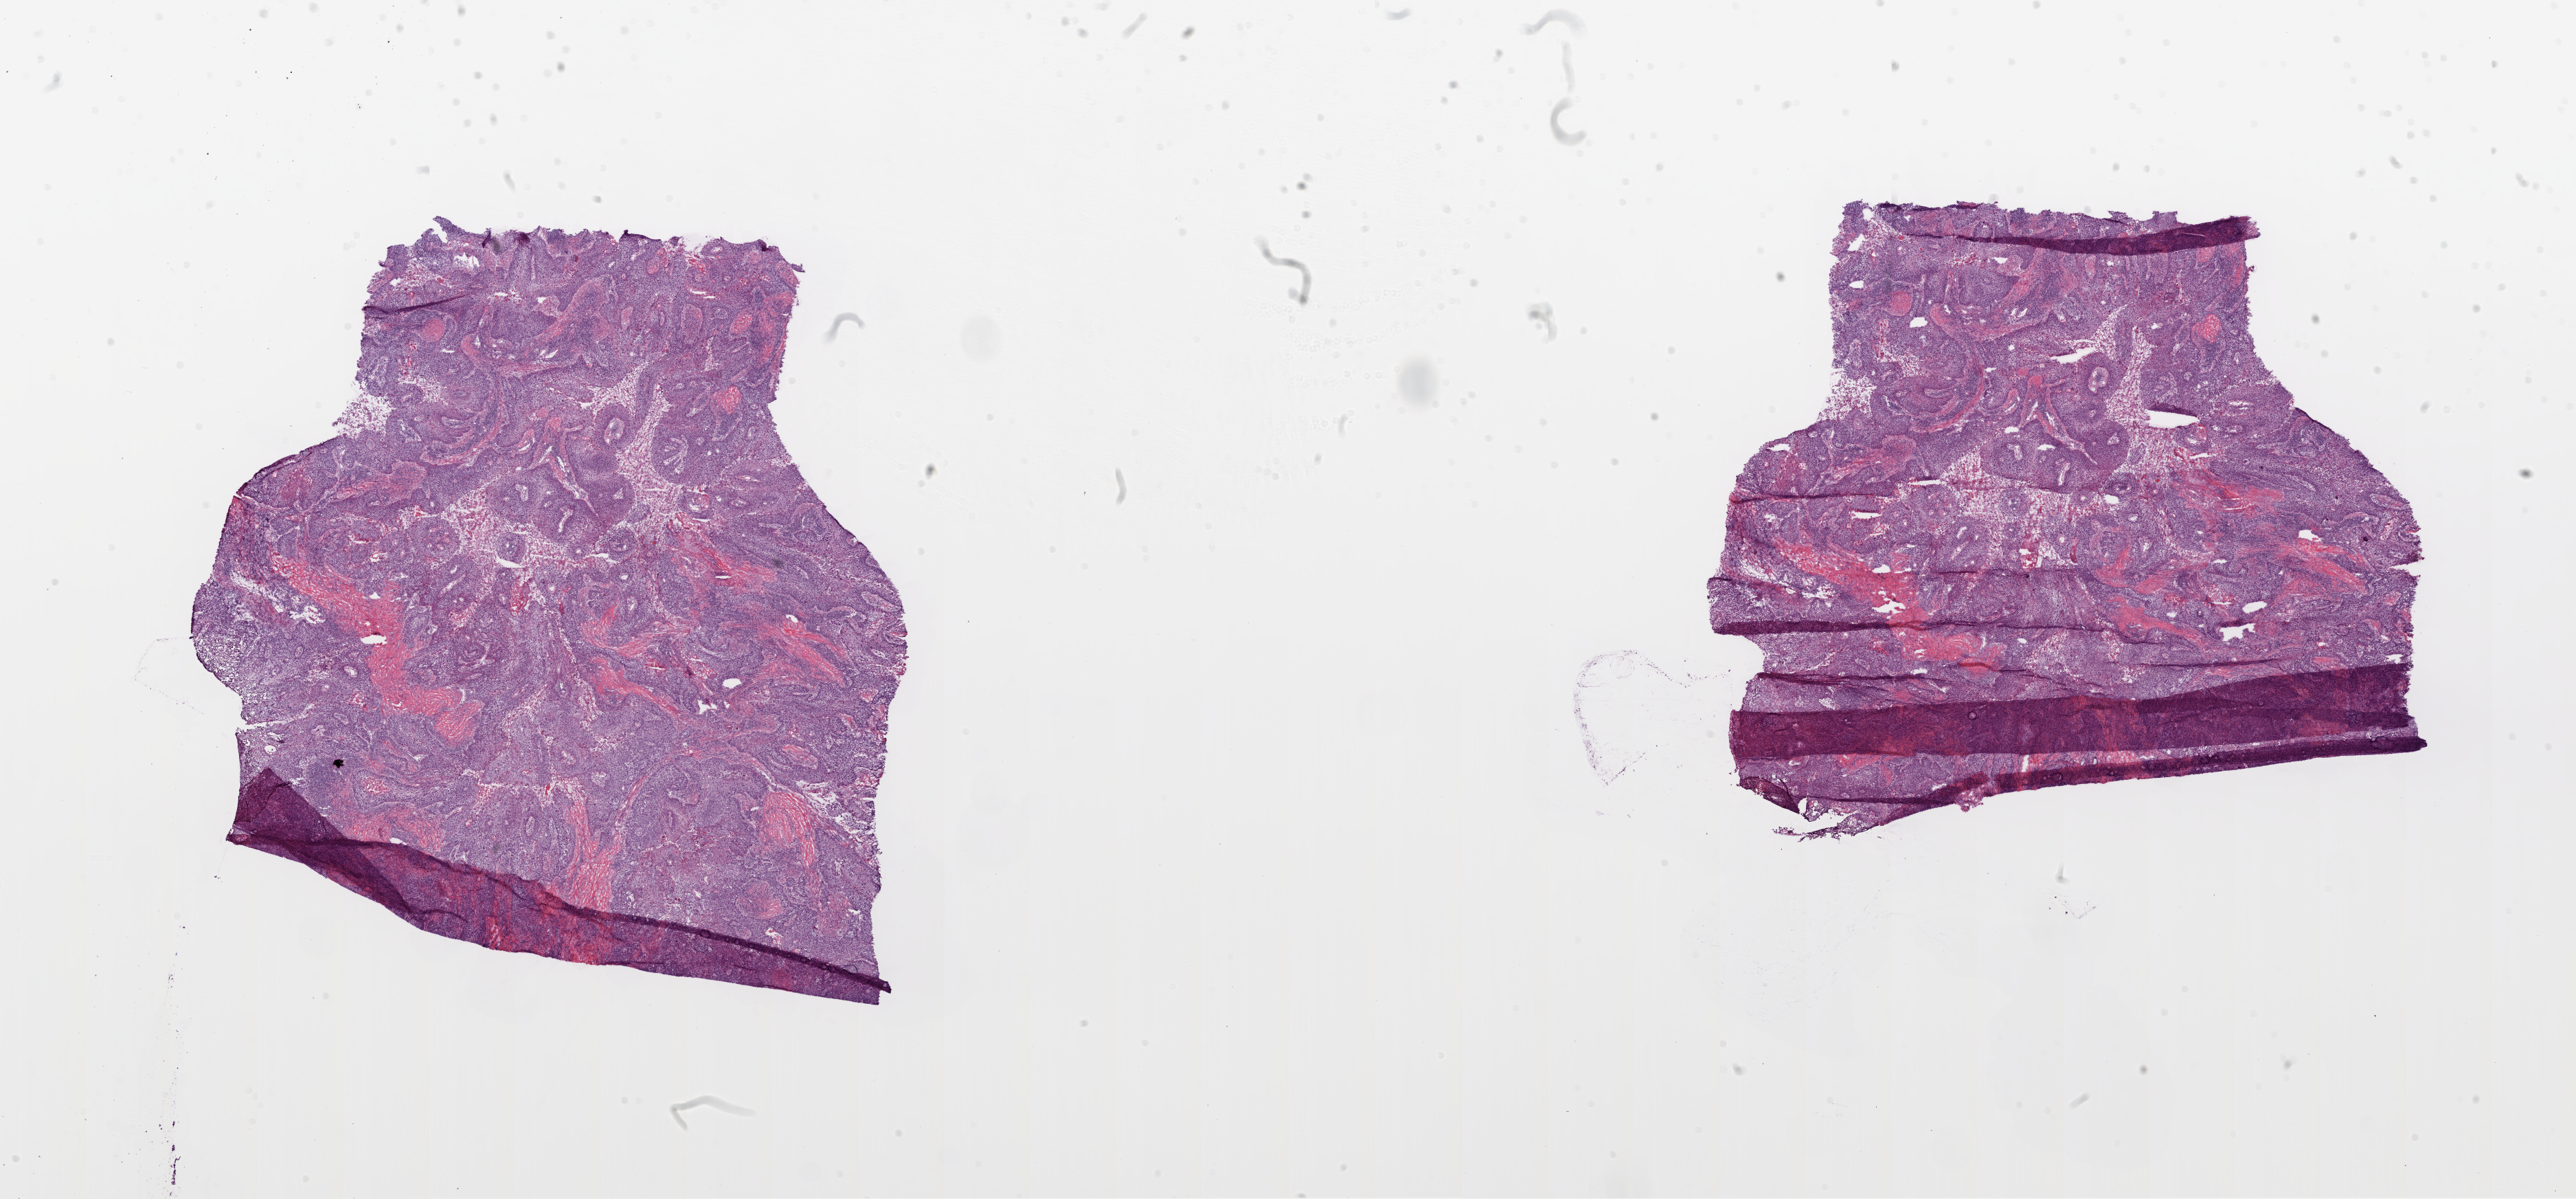
Digitized H&E tissue section (whole slide) — shown as a low-resolution overview of the whole scanned area (about 30.1 x 14.0 mm, from a 20x scan), frozen section from the bottom of the tissue portion, sample: primary tumour, lung. Male patient; age at initial diagnosis 66 years. Pathologist review of this section (percent, as recorded): tumour cells 70%, tumour nuclei 80%, normal cells 0%, stromal cells 15%, necrosis 15%.
AJCC pathologic stage: IIIA (5th edition). Pathologic diagnosis: Squamous cell carcinoma, NOS (lower lobe, lung).